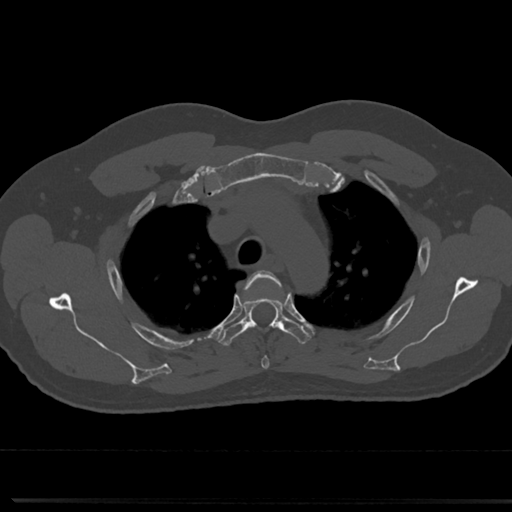
CT including the spine, one axial slice; reconstruction kernel Br40s/3; bone window (W 1800 / L 400 HU); 0.5 mm slice thickness; 512 × 512 image matrix, field of view 355 × 355 mm. Male patient, age 61 years. From the clinical record (not read from this slice): primary cancer: prostate.
Structures marked on this image (semi-automatic segmentation, software-assisted and operator-edited):
- T3 vertebra: bounding box [x1, y1, x2, y2] px = [252, 271, 290, 368]
- T4 vertebra: [219, 274, 311, 346]